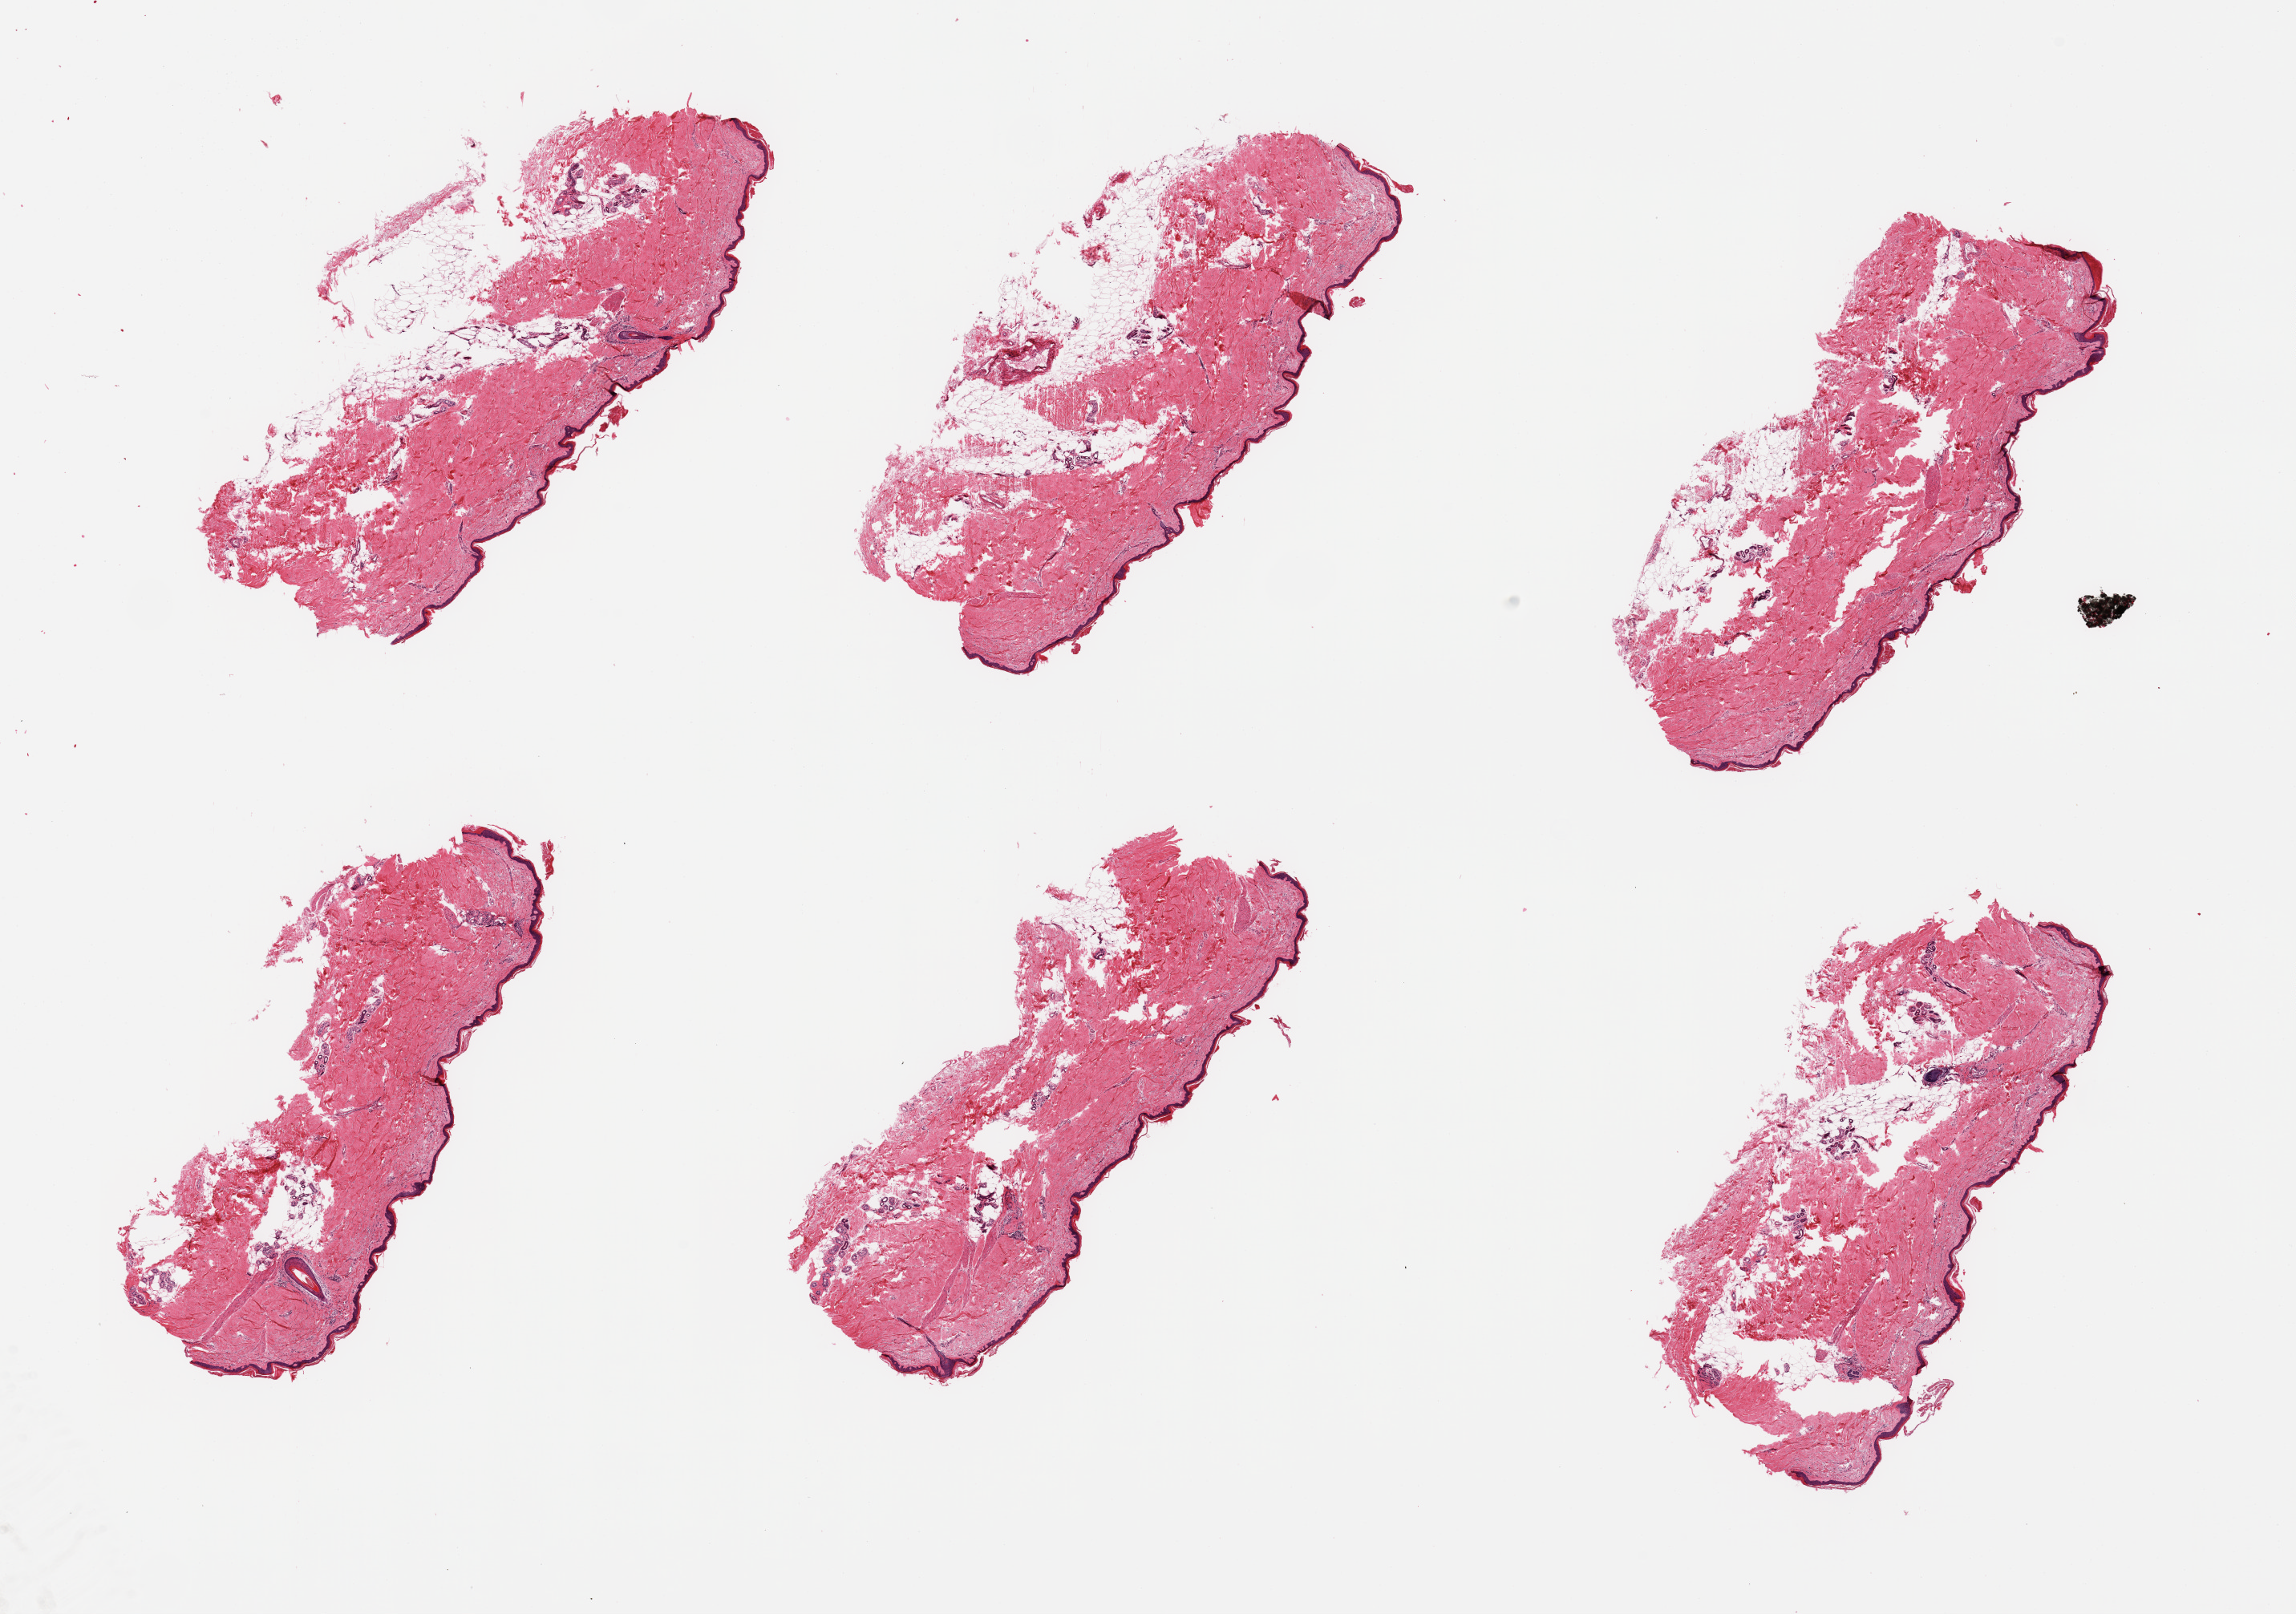
Whole-slide image, hematoxylin and eosin (H&E) stain, brightfield — shown as a low-resolution overview of the whole scanned area (about 22.6 x 15.9 mm); PAXgene-fixed, paraffin-embedded tissue; sampled site (target tissue): skin of lower leg; donor tissue sample. Donor: male.
Review note (as recorded): 6 fragmented pieces; 1 mm subcutaneous fat on 3 of 6 pieces.